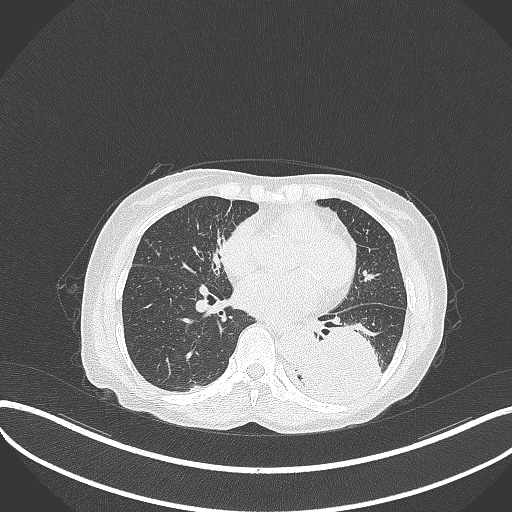
Chest CT, one axial slice. Slice 134 of 370 in the series (ordered by position). 120 kVp. Lung window (W 1500 / L -600 HU). 1 mm slice thickness. 512 × 512 image matrix. Patient: female, 78 years. Case-level facts recorded for this patient, not image findings: clinical TNM (as recorded): T3 N0 M1.
Annotated regions visible in this slice (bounding box drawn by a radiologist):
- lung tumour (recorded histology: squamous cell carcinoma): bounding box <301,328,387,411> (left, top, right, bottom; pixels)